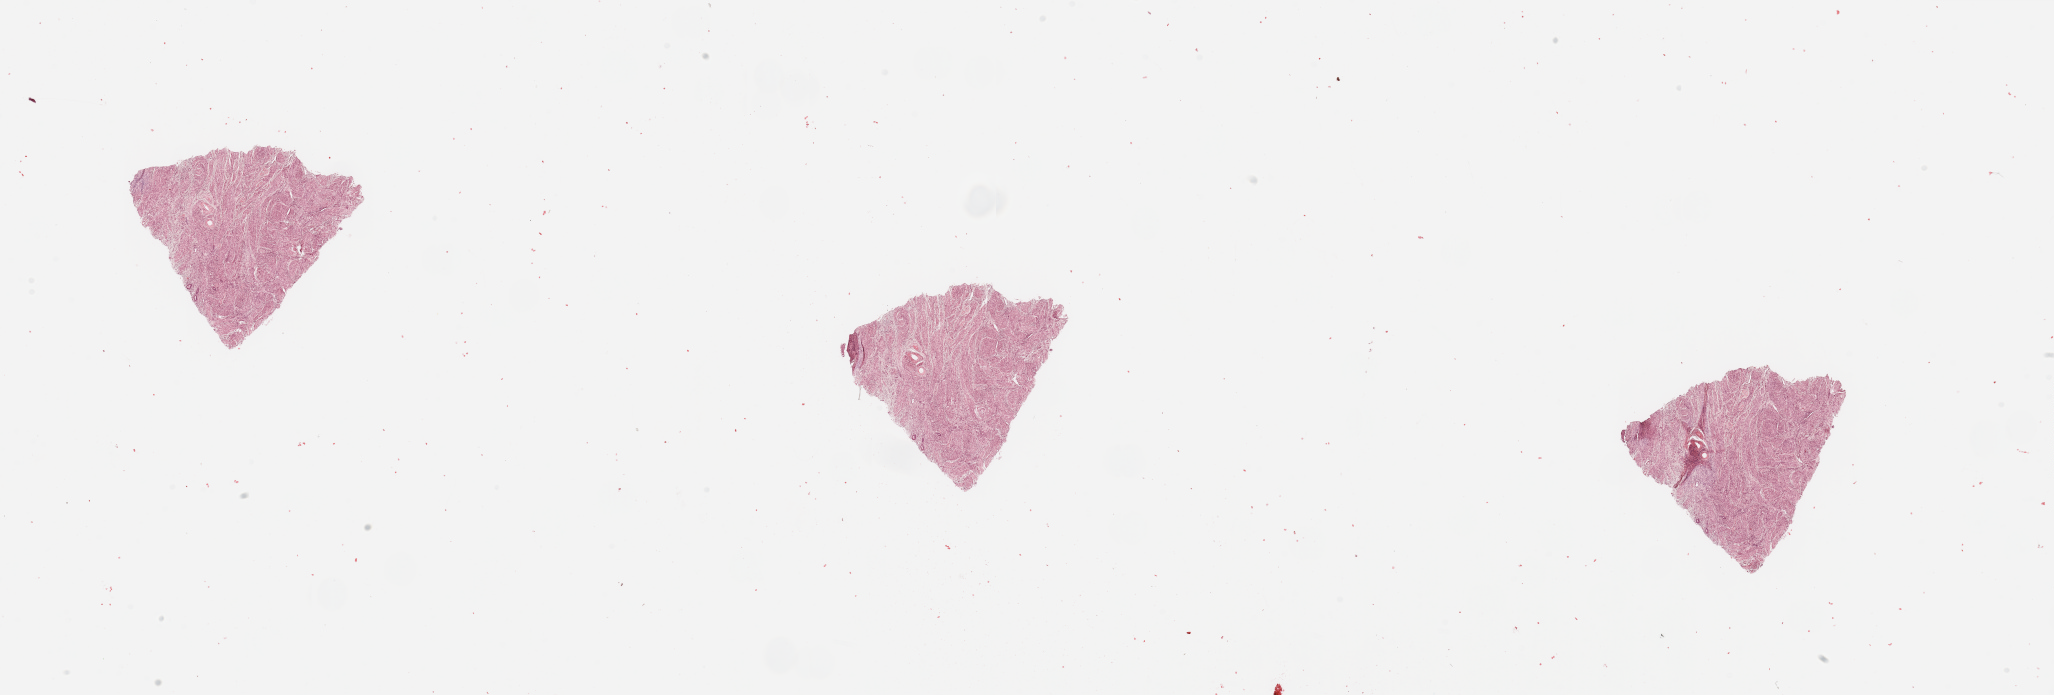
Digitized Hematoxylin and eosin (H&E) stained tissue section (whole slide) — a low-resolution overview of the entire scanned area, about 32.5 x 11.0 mm, normal (non-tumour) tissue sample, uterus. Patient: female, age 63 years.
This section: normal (non-tumour) tissue from the same patient. Patient diagnosis: Endometrioid adenocarcinoma, NOS.